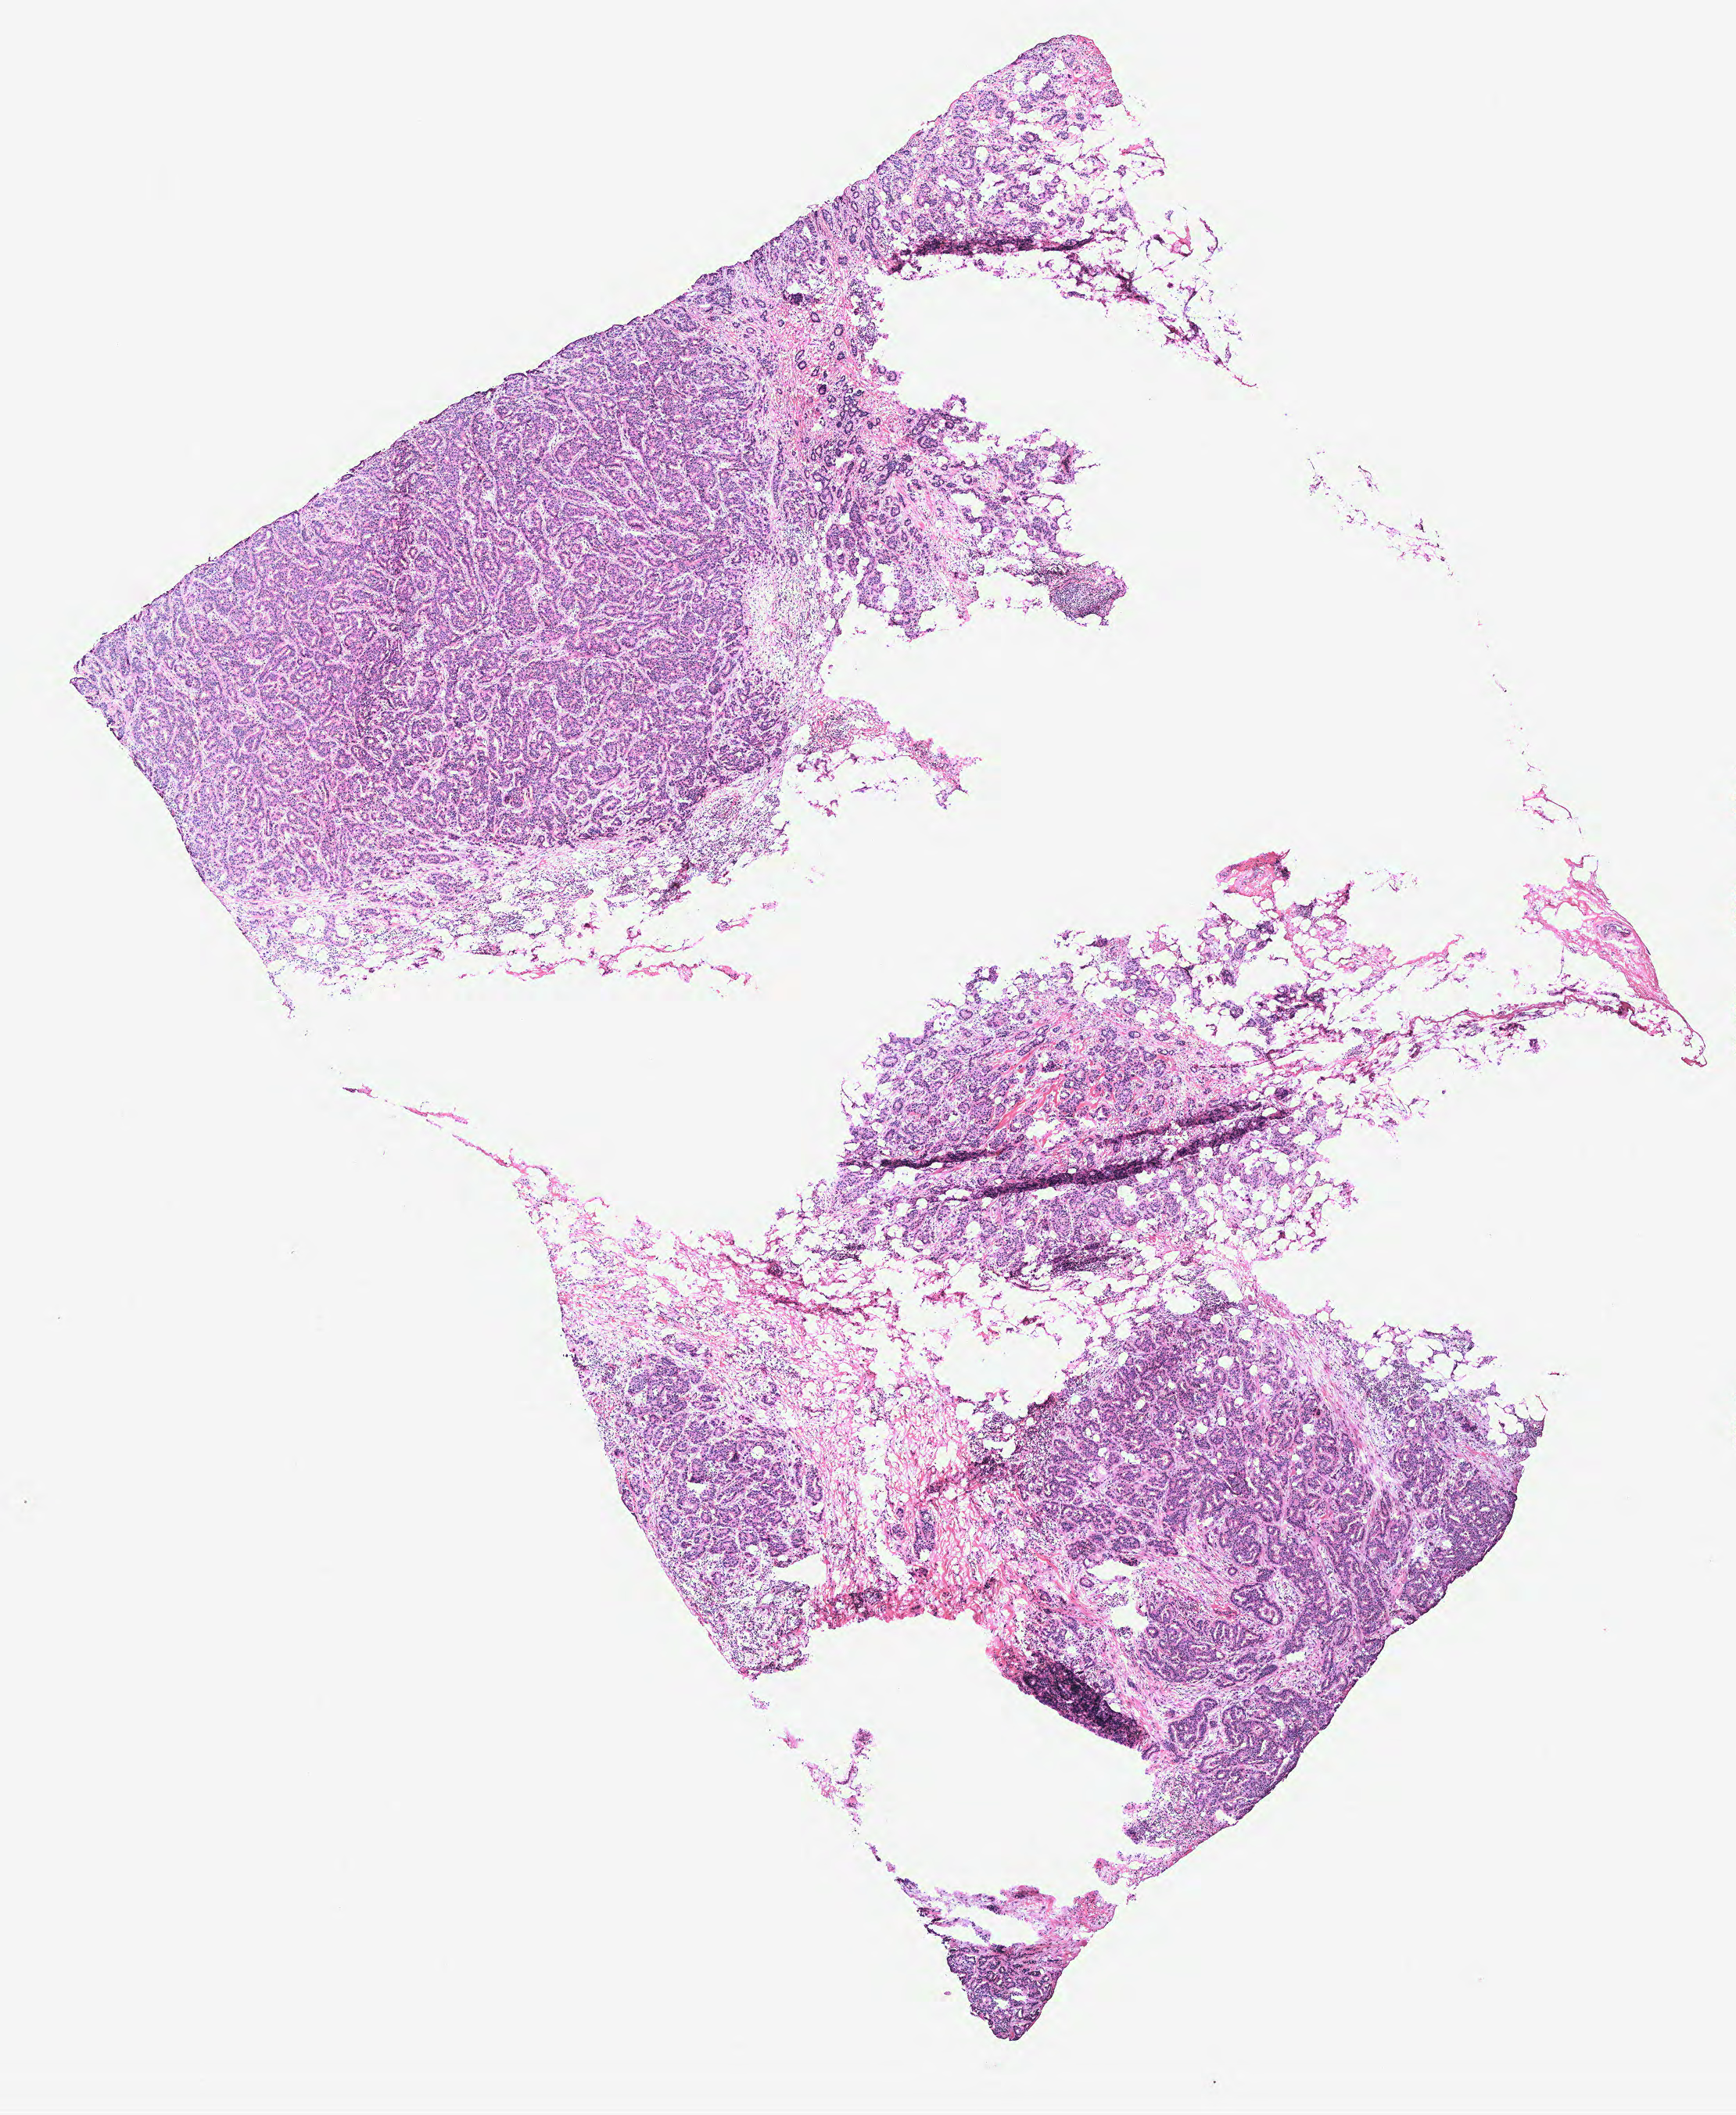
Hematoxylin and eosin (H&E) stained whole-slide image, low-resolution overview of the scanned area, about 8.9 x 10.8 mm; tumour tissue sample, breast. 55-year-old female patient.
Diagnosis: Infiltrating duct carcinoma, NOS. AJCC pathologic stage: IIIA.